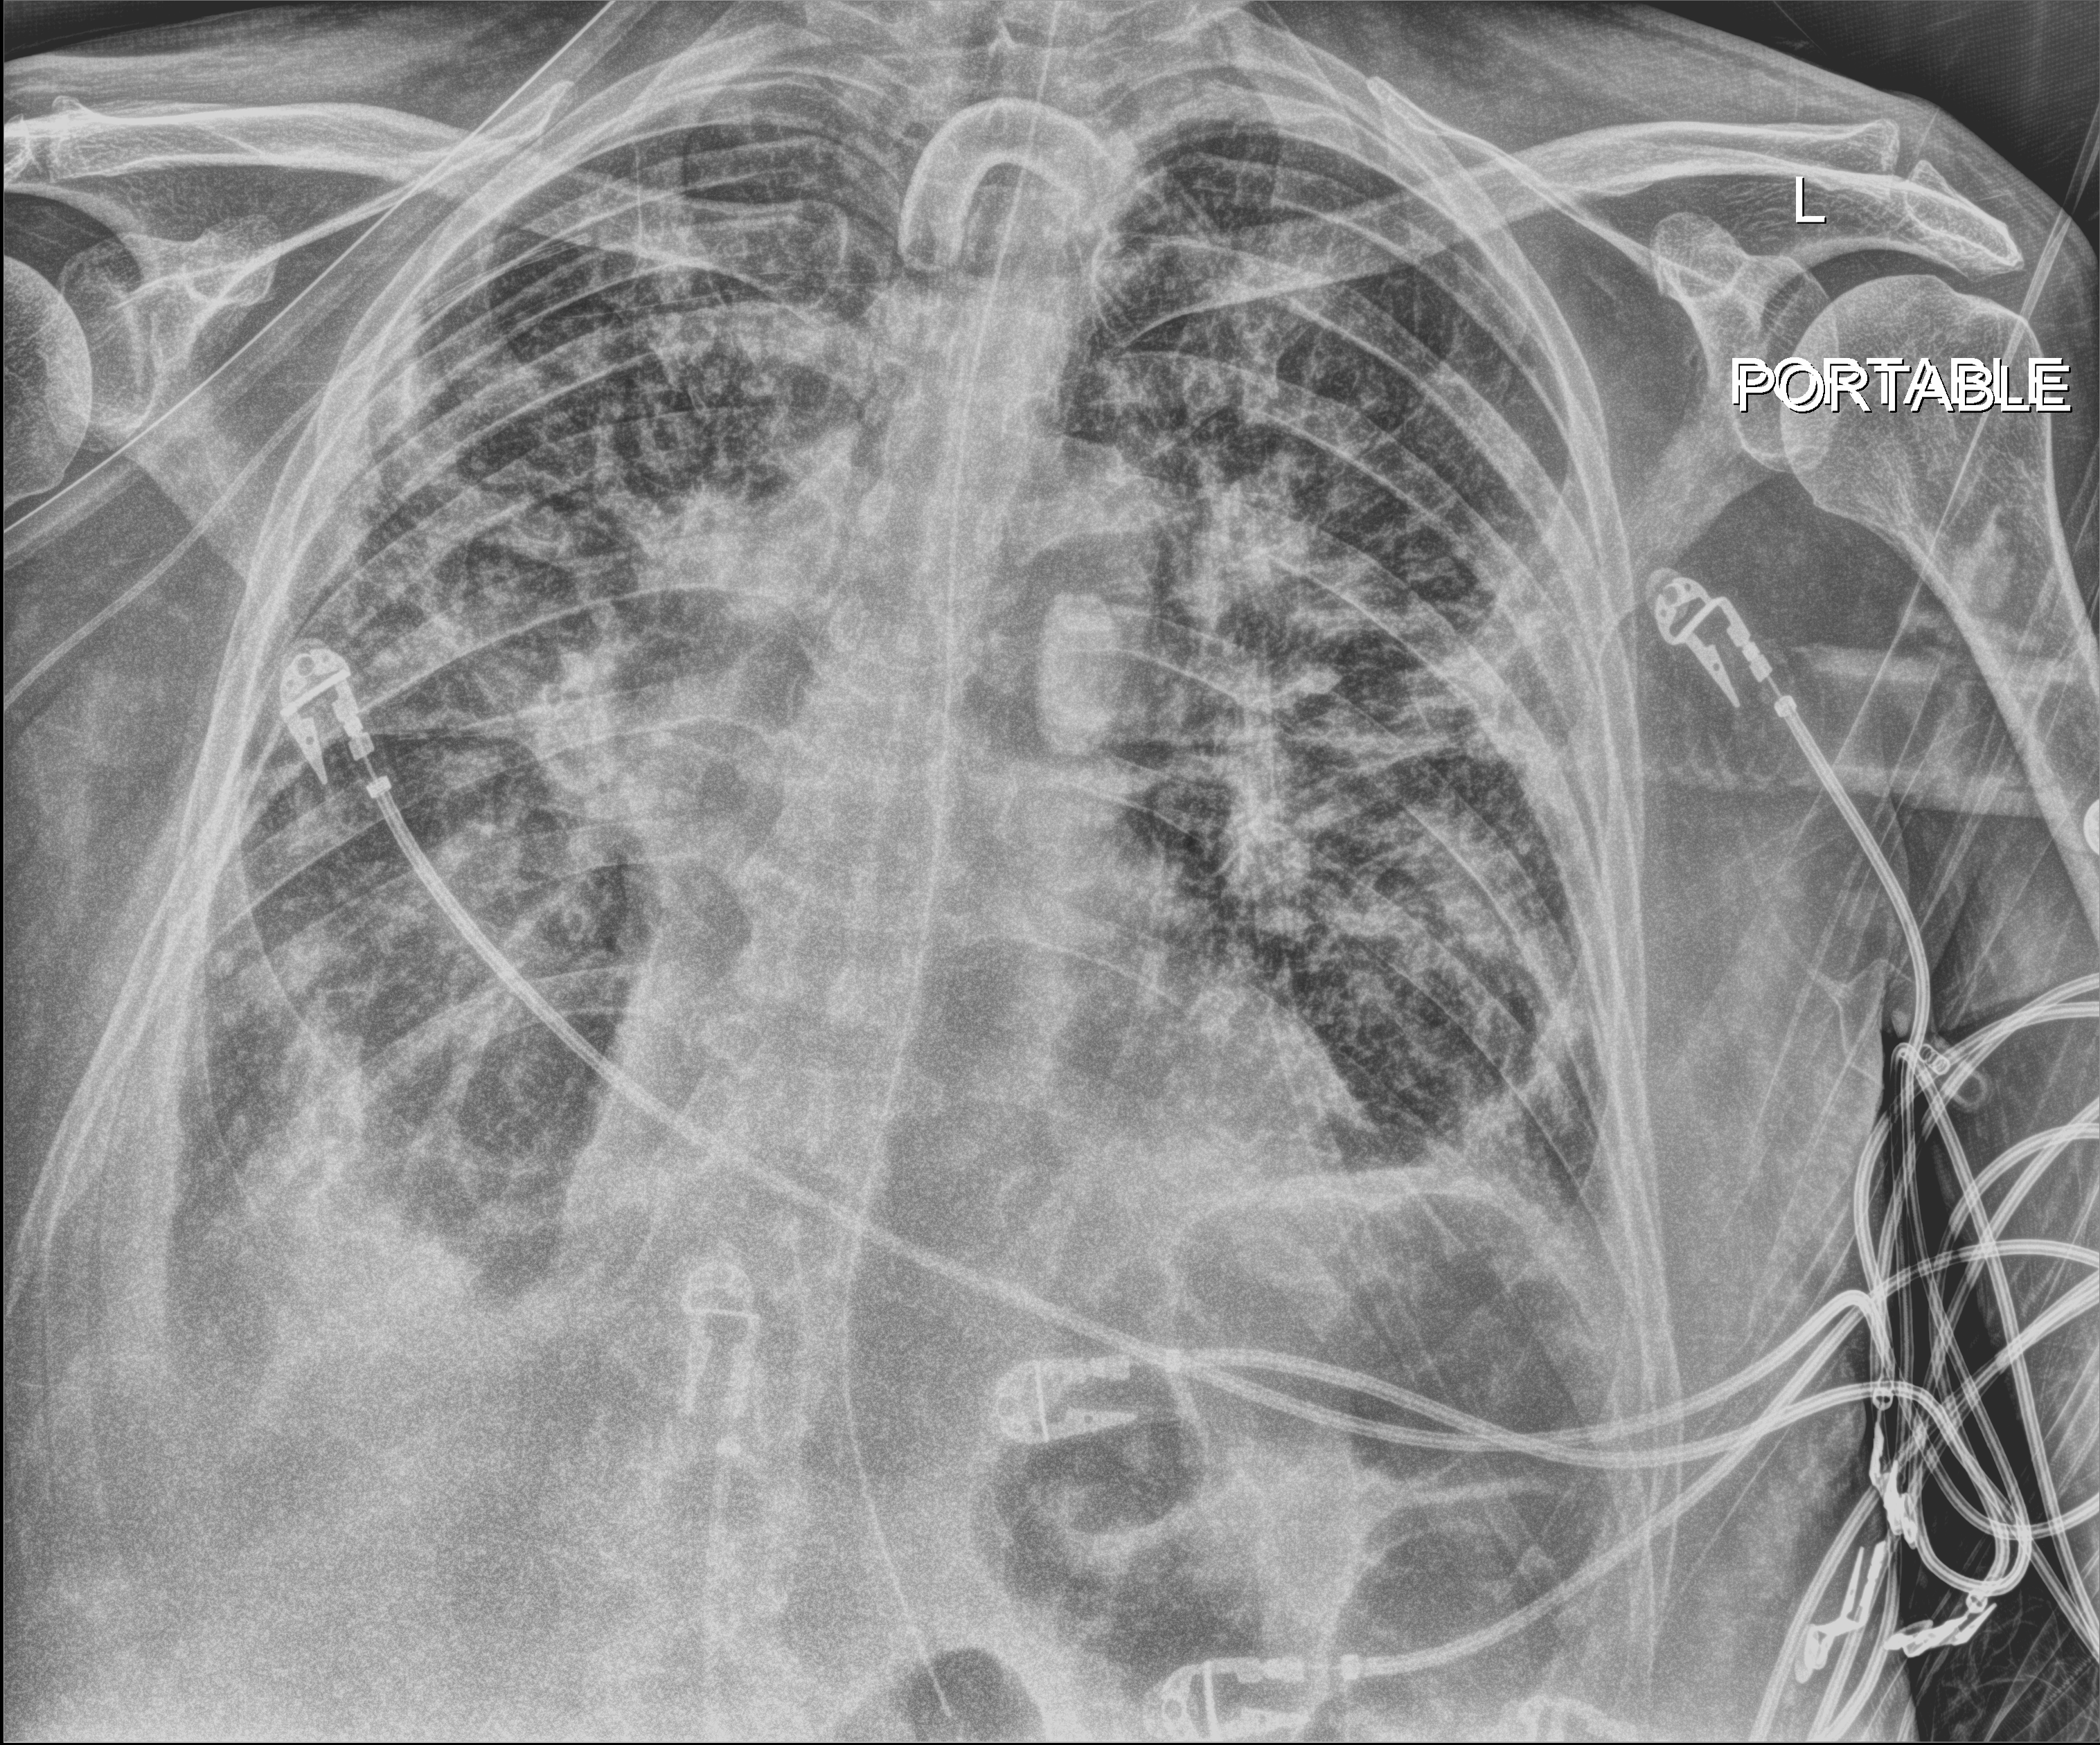
Bedside chest radiograph (digital radiography), anteroposterior (AP) projection. Patient hospitalised with COVID-19; male, aged 75–90 years.
Admission-level facts for this patient (not findings on this image; timing relative to this image not recorded):
- mechanically ventilated during this hospital stay: yes